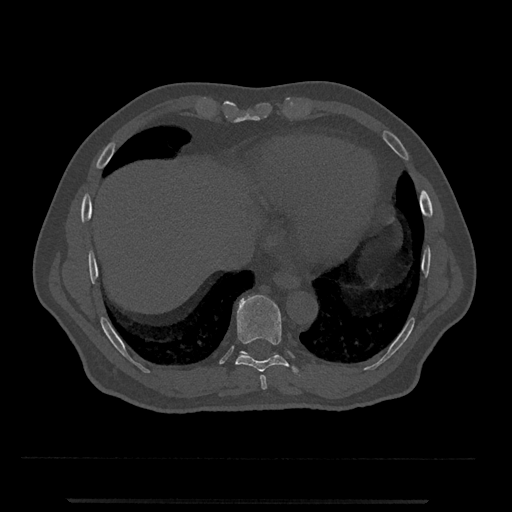
CT including the spine, one axial slice. Position 567 of 797 along the scan axis. Reconstruction kernel Br40s/3. Bone window (W 1800 / L 400 HU). 512 × 512 image matrix, field of view 419 × 419 mm. Male patient, age 63 years. From the clinical record (not read from this slice): primary cancer: prostate.
Outlined on this slice (semi-automatic segmentation, software-assisted and operator-edited):
- T10 vertebra: bounding box (x1, y1, x2, y2) in pixels: (240, 351, 278, 356)
- T8 vertebra: (260, 375, 267, 390)
- T9 vertebra: (235, 295, 299, 375)